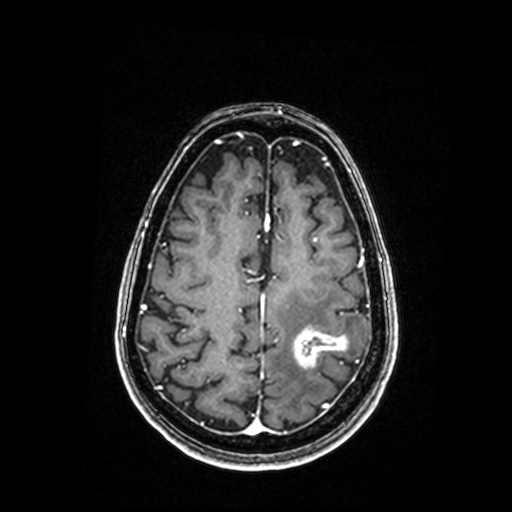
Brain MRI from a brain-tumour surgery series, one axial slice; slice 58 of 192 in the series (ordered by position); T1-weighted post-contrast; 512 × 512 image matrix, field of view 250 × 250 mm. From the clinical record (not read from this slice): histopathology: Metastastic Carcinoma, Poorly Differentiated.
Outlined on this slice (manually delineated by an expert):
- tumour: box from (x=293, y=331) to (x=347, y=368) px